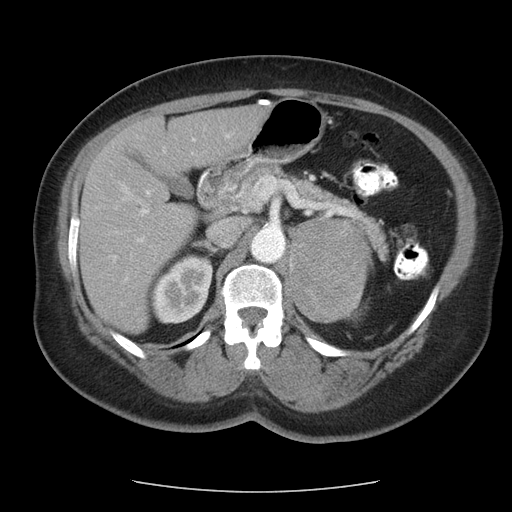
Contrast-enhanced abdominal CT, one axial slice; slice 66 of 95 in the series (ordered by position); intravenous contrast given; soft-tissue window (W 400 / L 40 HU); 5 mm slice thickness; 512 × 512 image matrix, field of view 362 × 362 mm. Patient: female, 71 years. From the clinical record (not read from this slice): diagnosis: adrenocortical carcinoma; tumour side: left adrenal; tumour size at pathology: 8.8 cm; Ki-67 index: 20 %; stage (as recorded): 2.
Annotated regions visible in this slice (semi-automatic segmentation, software-assisted and operator-edited):
- mass: box from (x=289, y=218) to (x=369, y=320) px